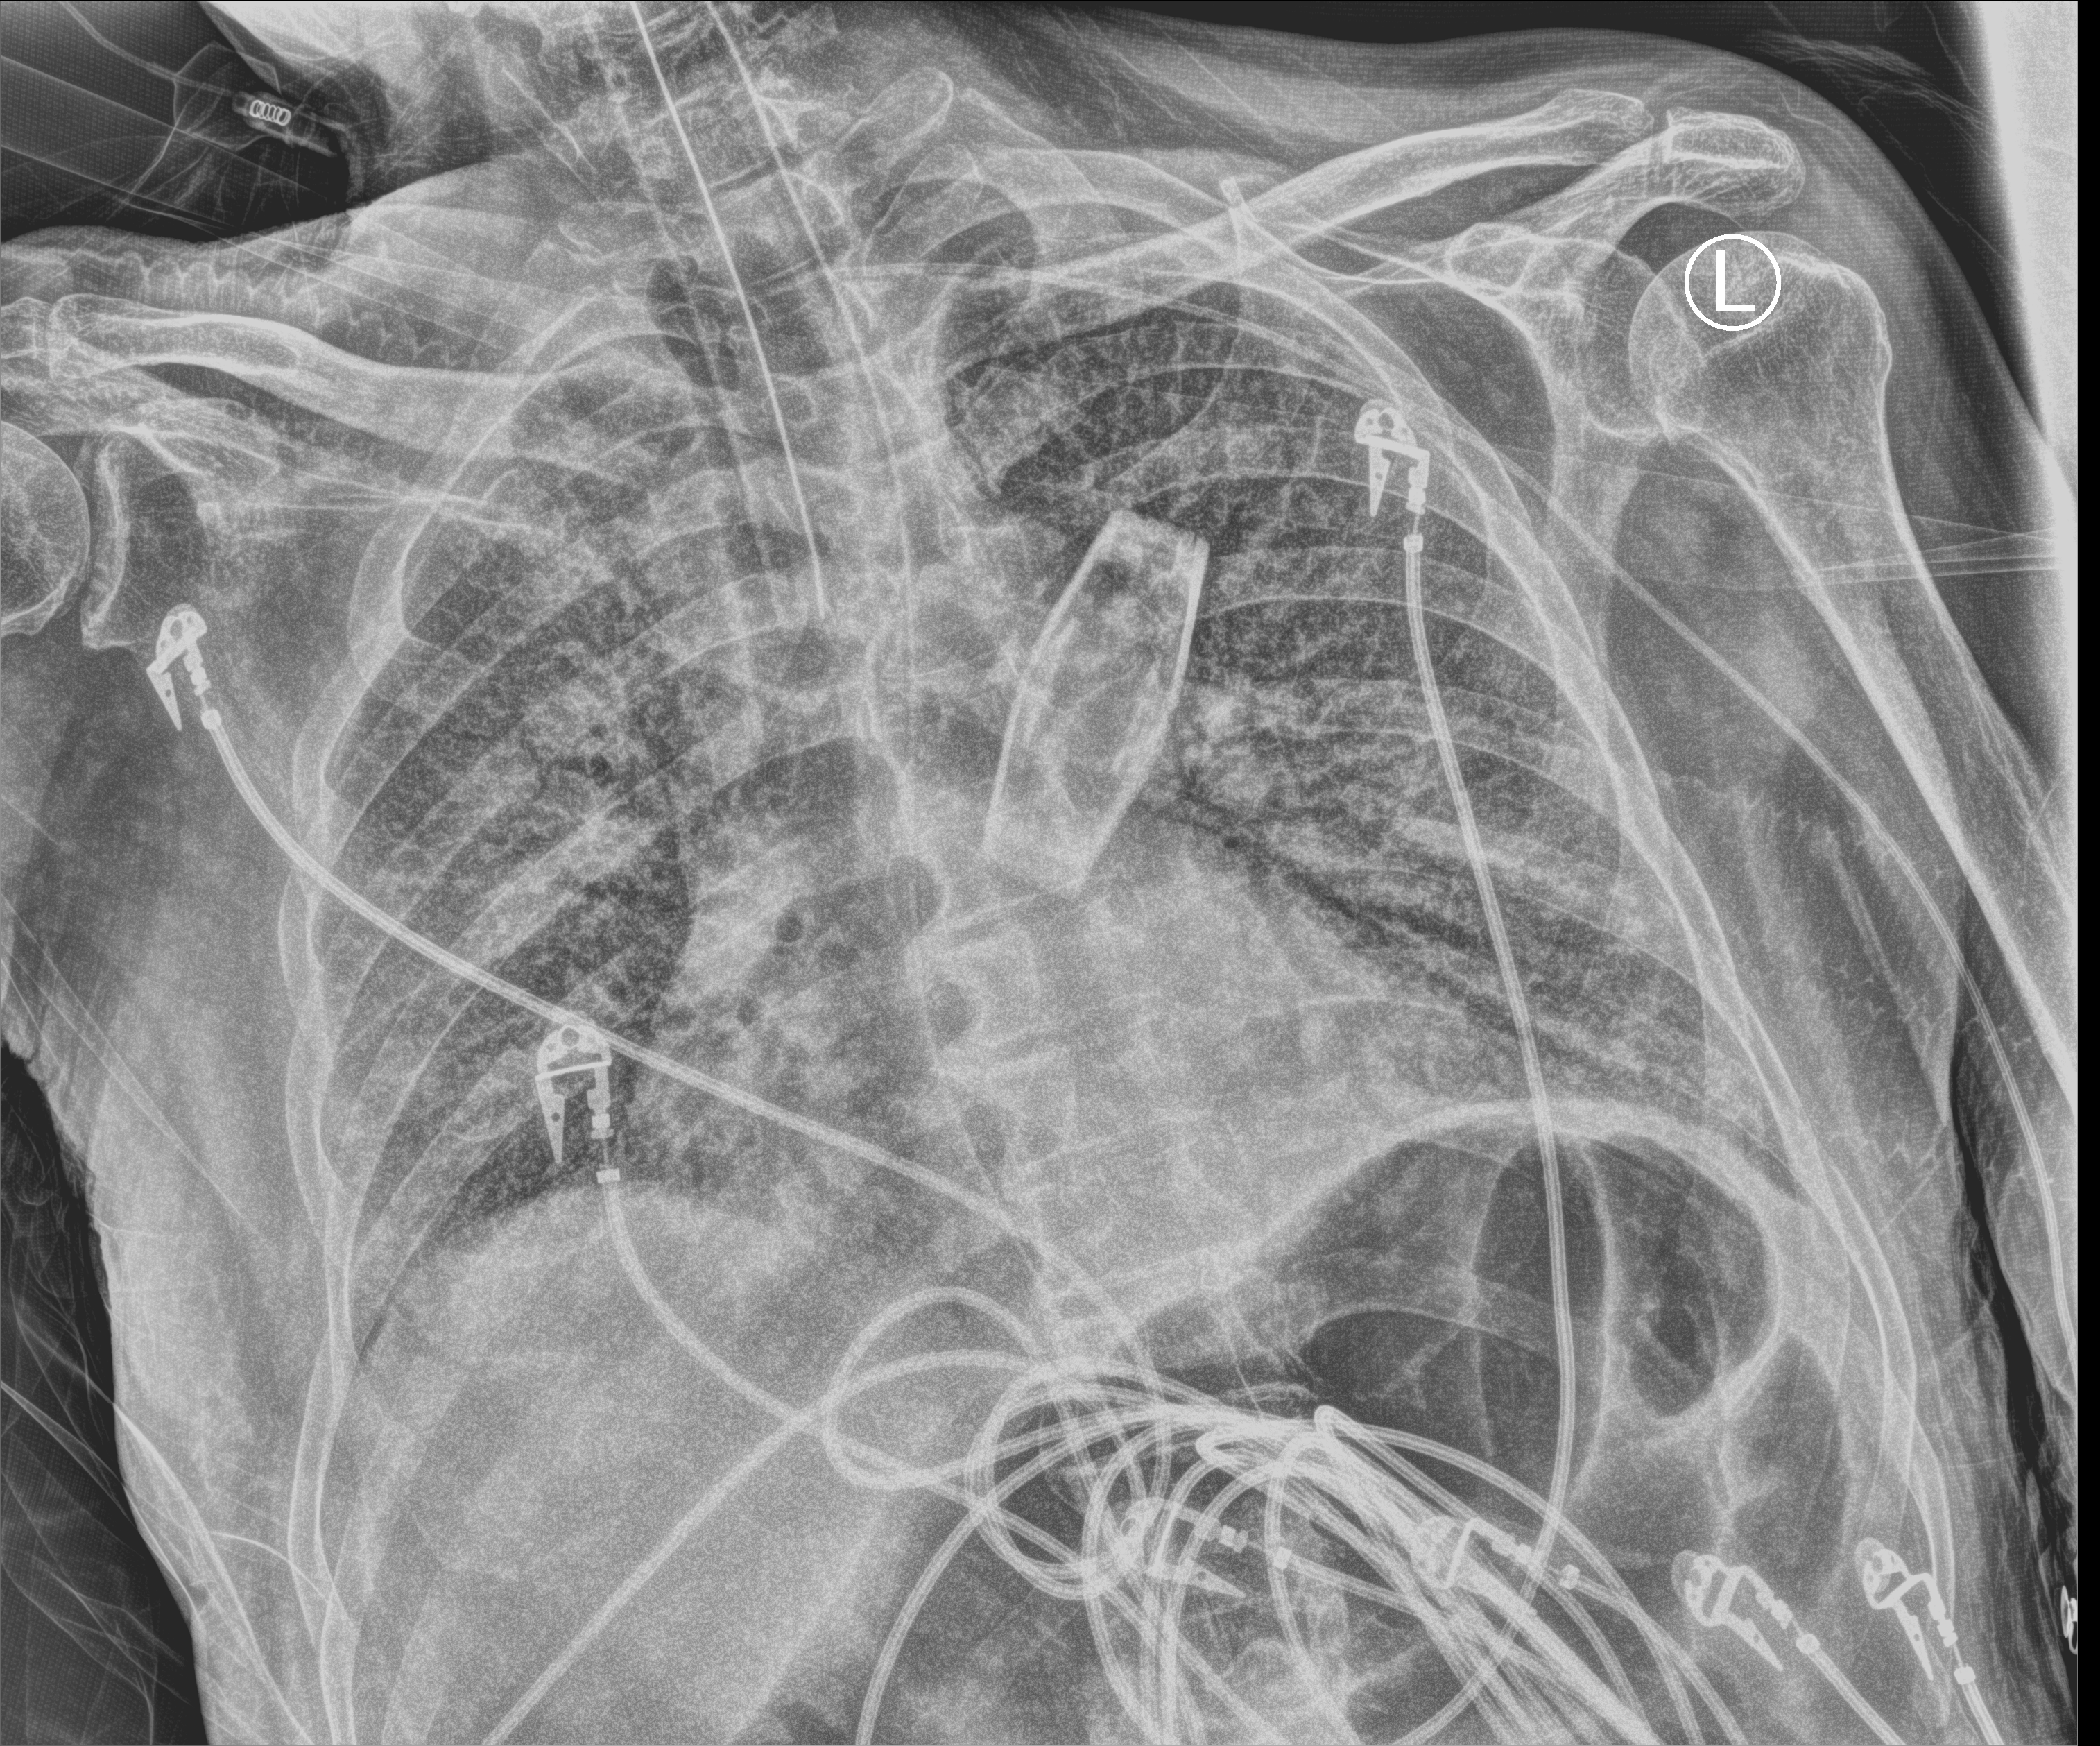
Chest X-ray (portable); anteroposterior (AP) projection. Patient hospitalised with COVID-19; male, aged 75–90 years.
Admission-level facts for this patient (not findings on this image; timing relative to this image not recorded): length of hospital stay: 30 days; mechanically ventilated during this hospital stay: yes; chronic kidney disease (admission record): no.